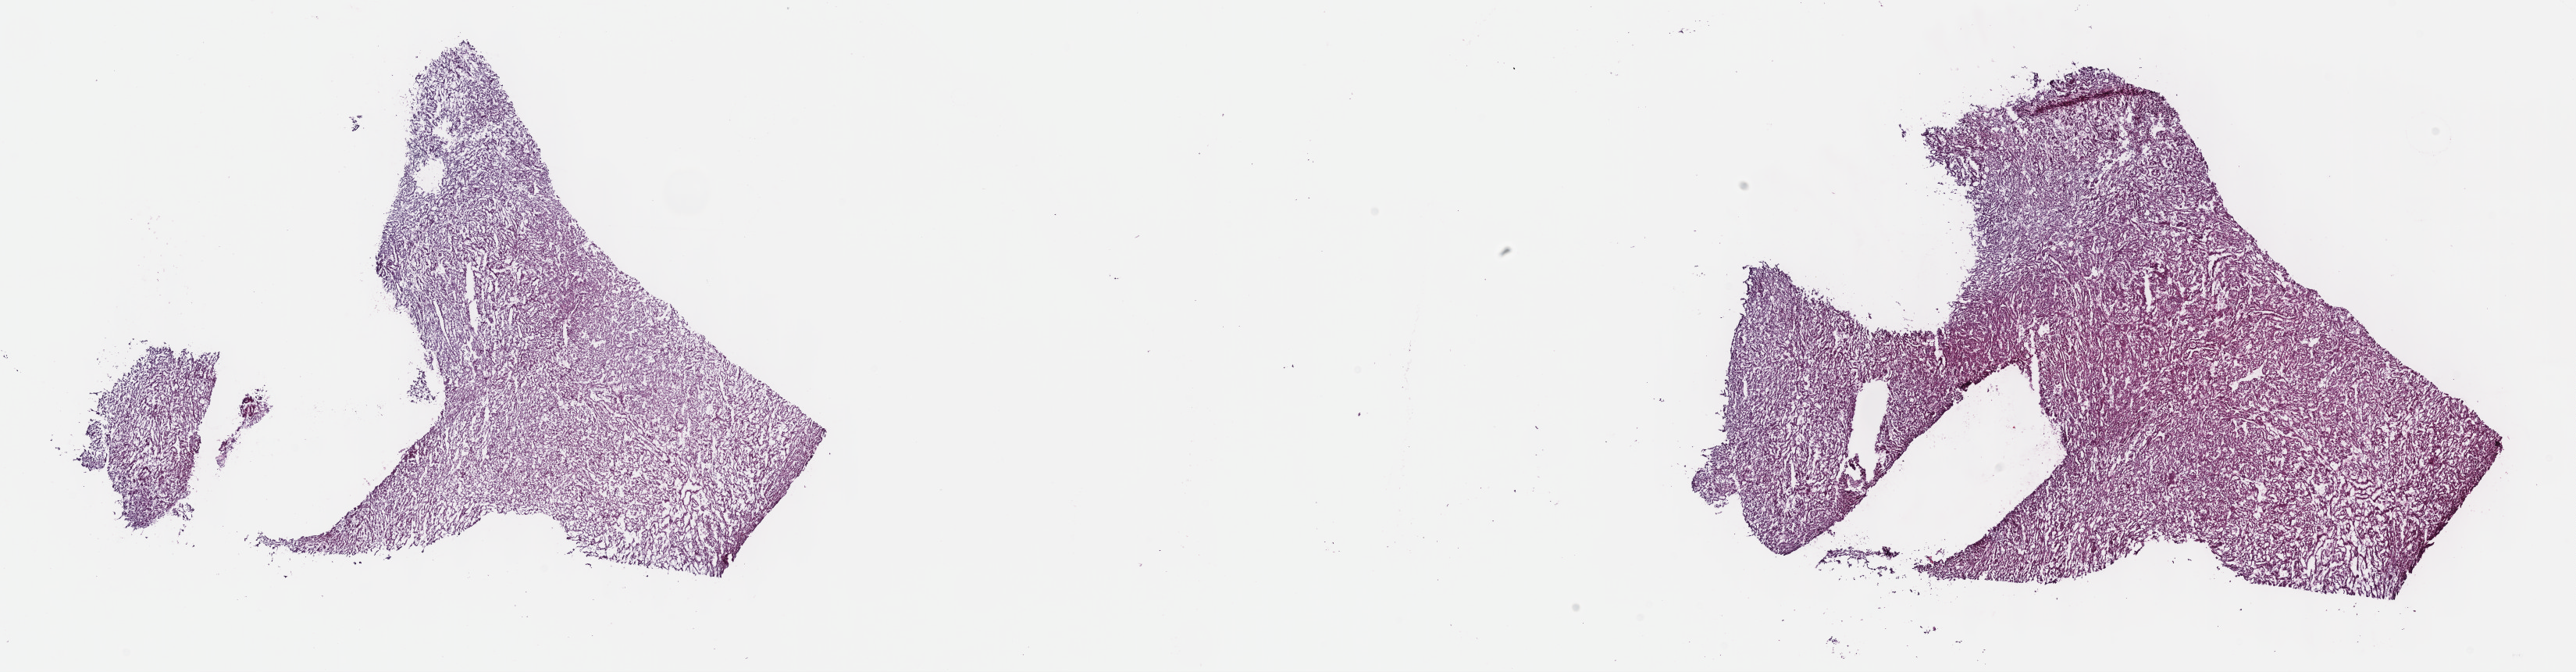
Digitized H&E-stained tissue section (whole slide) — shown as a low-resolution overview of the whole scanned area (about 26.7 x 7.0 mm, slide scanned at 40x); frozen section from the top of the tissue portion; sample: primary tumour, kidney. Patient: female, age at initial diagnosis 37 years. Pathologist review of this section (percent, as recorded): tumour cells 90%, tumour nuclei 95%, normal cells 0%, stromal cells 10%, necrosis 0%. Inflammatory infiltration, as recorded: lymphocyte infiltration 0%, monocyte infiltration 0%, neutrophil infiltration 0%.
* diagnosis: Papillary adenocarcinoma, NOS
* AJCC pathologic stage: I